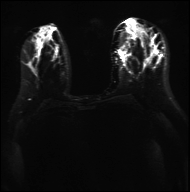
Breast MRI, one axial slice; slice 12 of 36 in the series (ordered by position); diffusion-weighted series; image 2 of 4 stored at this slice position (different b-values; order by instance number); 3 T; 4 mm slice thickness; 190 × 192 image matrix, field of view 317 × 320 mm. Female patient.
Structures marked on this image (expert manual segmentation):
- tumour on diffusion-weighted imaging: bounding box (x1, y1, x2, y2) in pixels: (49, 48, 60, 54)